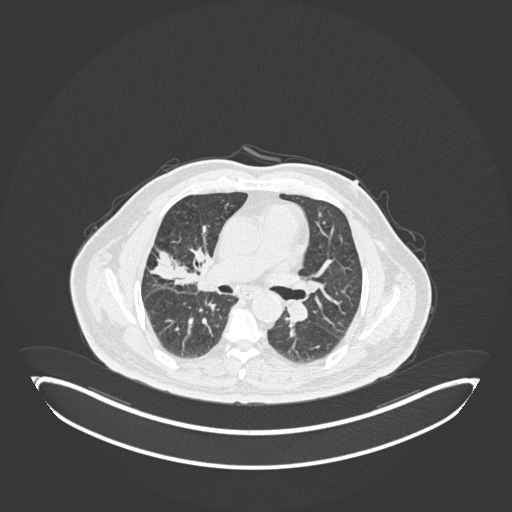
Chest CT, one axial slice; position 92 of 247 along the scan axis; reconstruction kernel B30f; 120 kVp; lung window (W 1500 / L -600 HU); 512 × 512 image matrix, field of view 500 × 500 mm. Patient: male, 72 years. From the clinical record (not read from this slice): clinical TNM (as recorded): T1c N0 M0.
Structures marked on this image (bounding box drawn by a radiologist):
- lung tumour (recorded histology: squamous cell carcinoma): bounding box <175,243,204,299> (left, top, right, bottom; pixels)